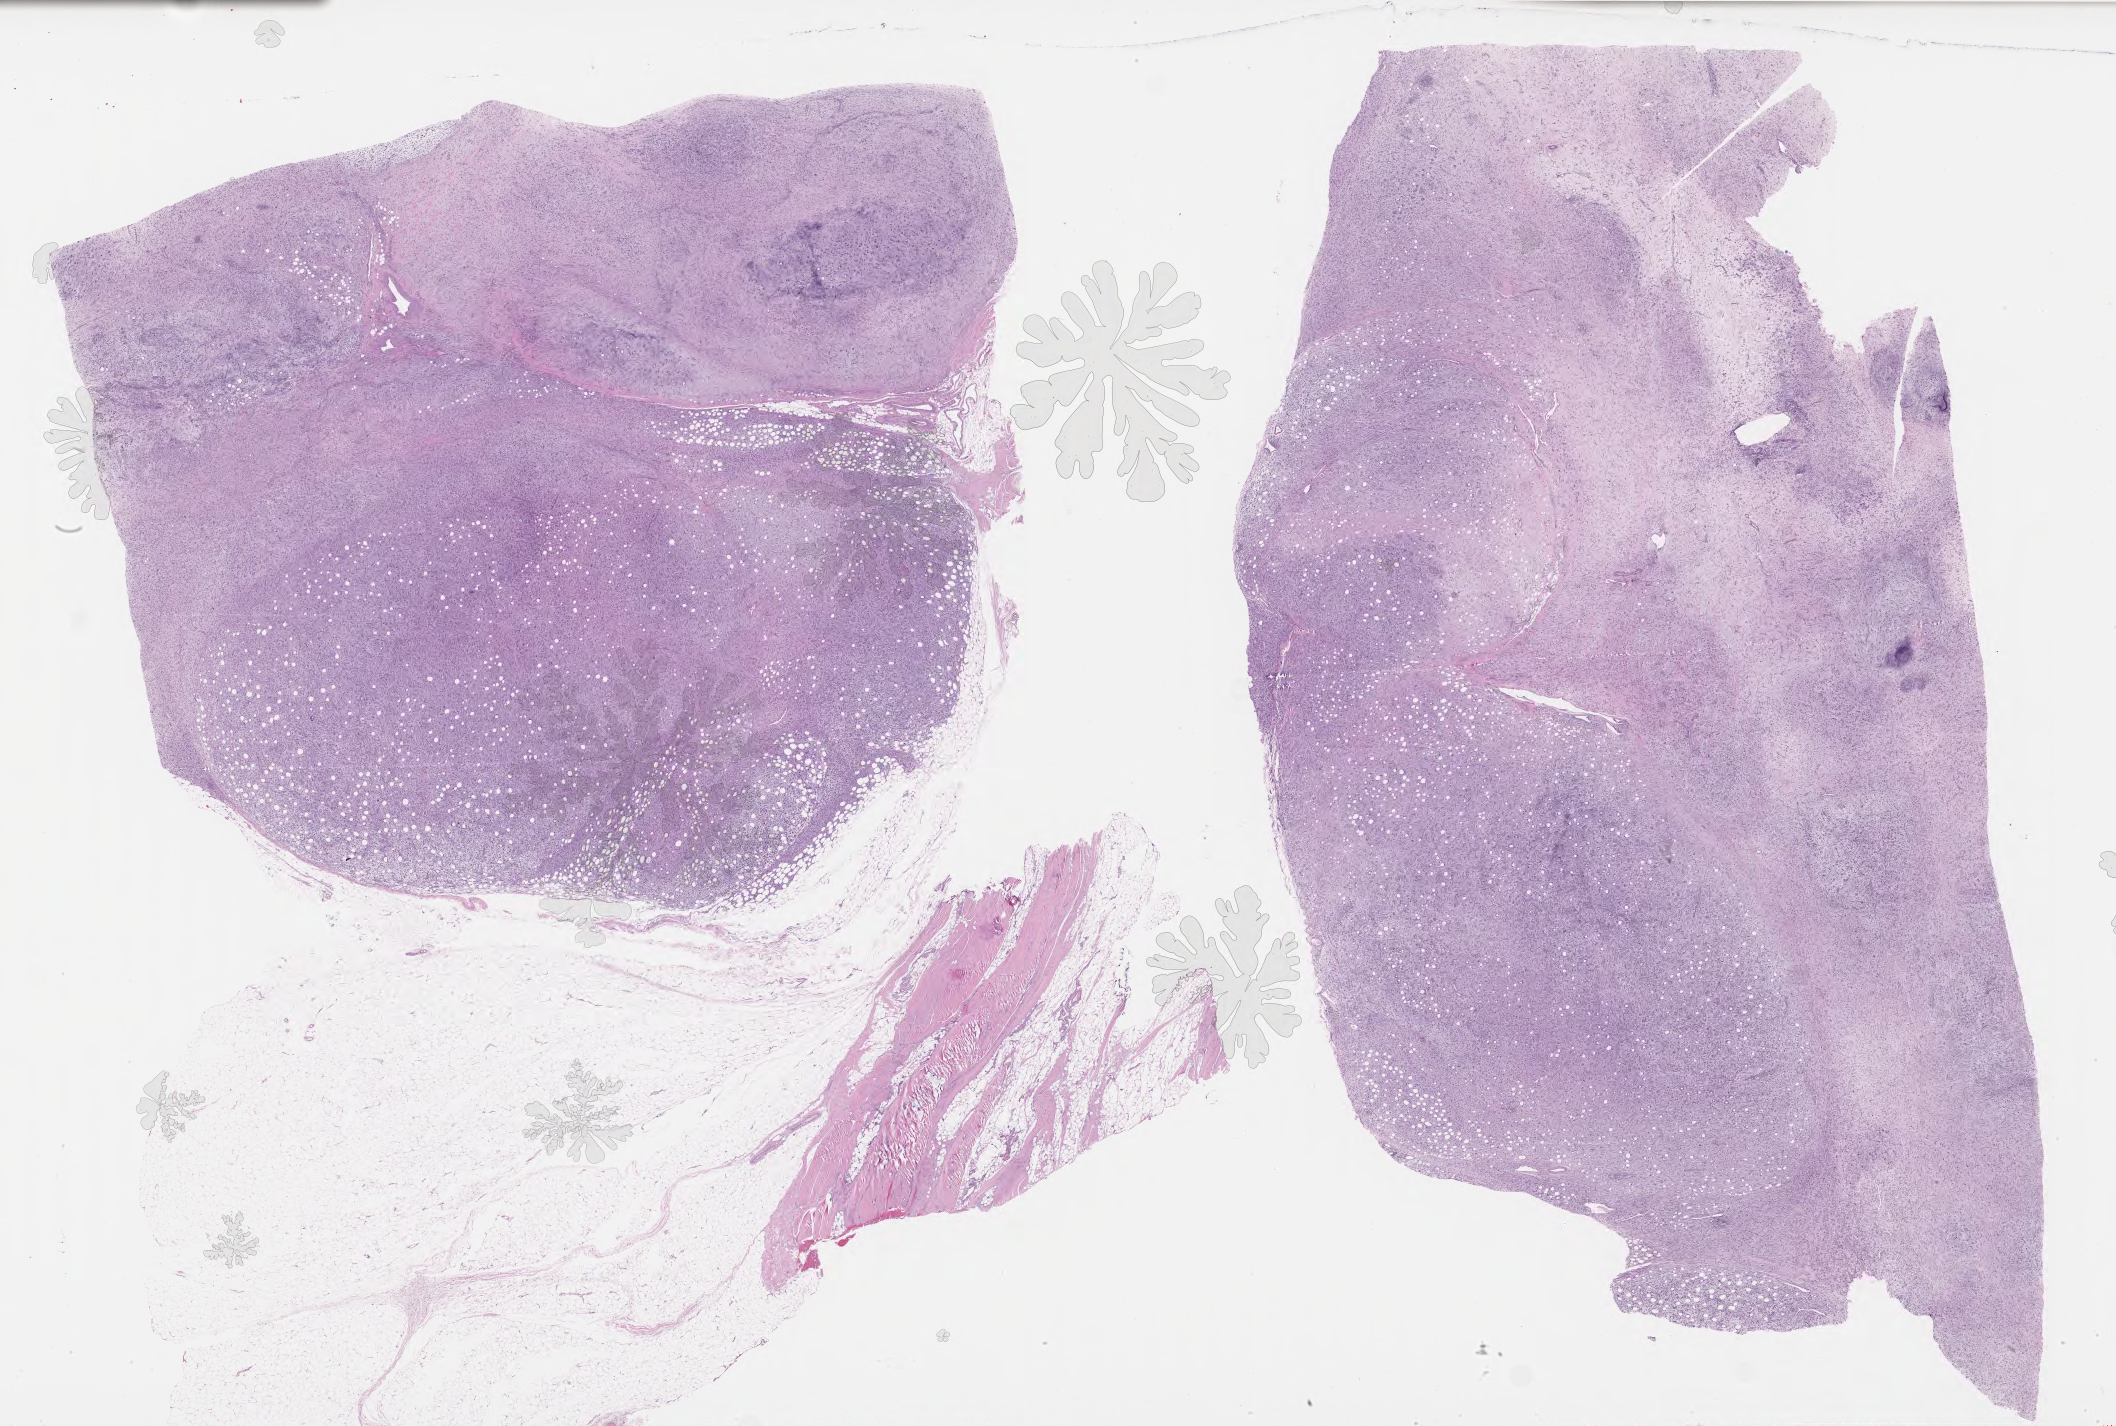
Whole-slide histology image, H&E-stained — shown as a low-resolution overview of the whole scanned area (about 34.2 x 23.1 mm, slide scanned at 40x); formalin-fixed paraffin-embedded (FFPE) diagnostic section; sample: primary tumour, connective, subcutaneous and other soft tissues. Female patient; age at initial diagnosis 86 years.
Histologic diagnosis: Fibromyxosarcoma (connective, subcutaneous and other soft tissues of pelvis).